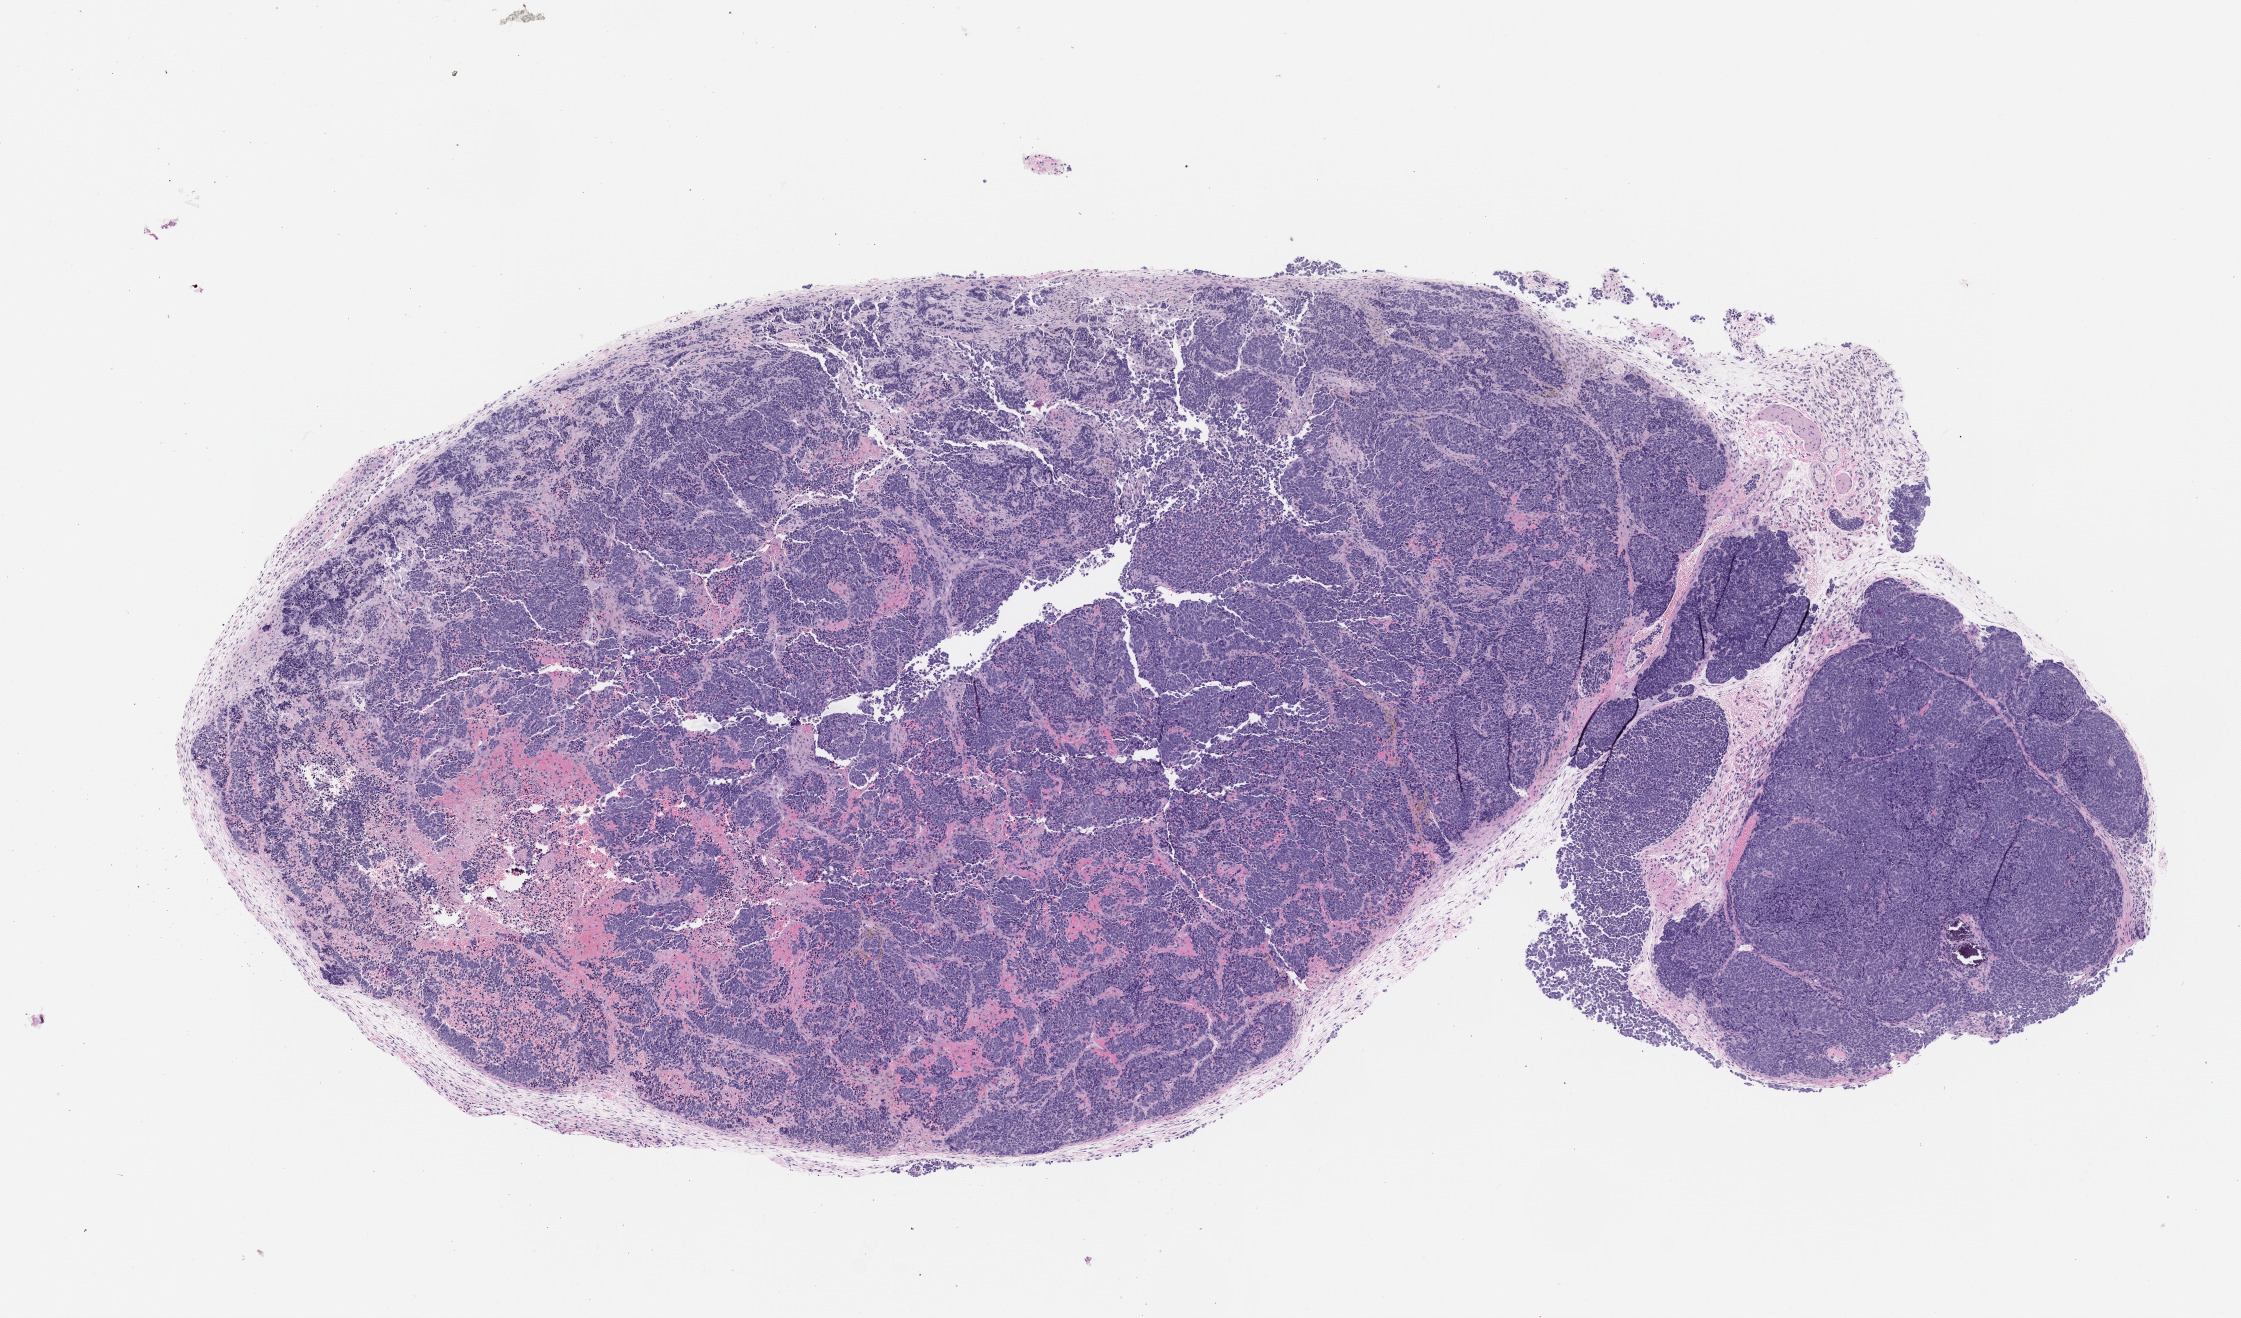
H&E whole-slide image of a patient-derived xenograft (PDX) tumor grown in a mouse, passage 2, low-resolution overview of the scanned area, about 9.0 x 5.3 mm. Formalin-fixed paraffin-embedded section. Originating tumor site category: bladder.
Originating patient diagnosis: Bladder Small Cell Neuroendocrine Carcinoma.